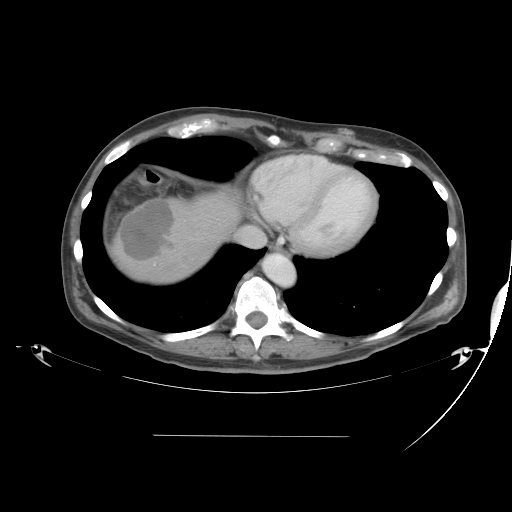
Contrast-enhanced abdominal CT, one axial slice; position 39 of 48 along the scan axis; reconstruction kernel STANDARD; intravenous contrast given; soft-tissue window (W 400 / L 40 HU); 512 × 512 image matrix, field of view 486 × 486 mm. Male patient, age 65 years. From the clinical record (not read from this slice): diagnosis: colorectal cancer liver metastases, imaged before liver resection; multiple liver metastases: yes; largest metastasis: 11 cm; disease in both lobes: yes.
Structures marked on this image (manually delineated by an expert):
- liver: box from (x=114, y=195) to (x=240, y=287) px
- planned liver remnant (the part of the liver to remain after resection): (x=207, y=194)–(x=240, y=222)
- liver metastasis: (x=120, y=199)–(x=173, y=260)